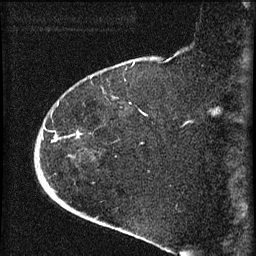
Breast MRI (dynamic contrast-enhanced), one sagittal slice. Position 16 of 60 along the scan axis. Dynamic contrast-enhanced series, image 2 of 4 at this slice position (ordered by acquisition). 1.5 T. TE 4.2 ms, TR 8.2 ms. 2 mm slice thickness. 256 × 256 image matrix, field of view 180 × 180 mm. Female patient, age 71 years.
Annotated regions visible in this slice (semi-automatically segmented with operator editing):
- analysis volume of interest (the breast-tissue region the enhancement analysis was run in; not a lesion): bounding box <35,75,123,190> (left, top, right, bottom; pixels)
- tumour enhancement mask (voxels above the 70 % enhancement threshold inside the analysis volume of interest): <55,135,57,141>